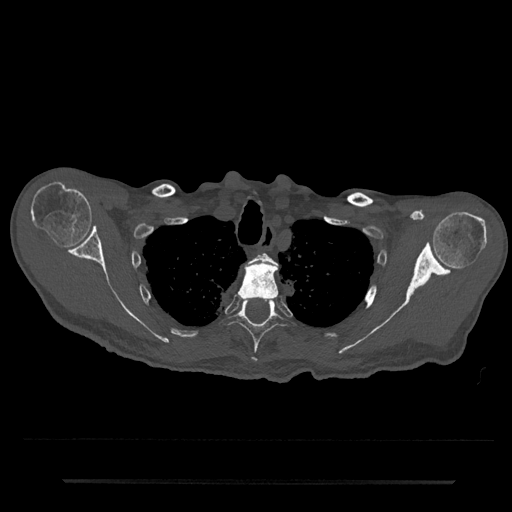
CT including the spine, one axial slice. Slice 637 of 797 in the series (ordered by position). Bone window (W 1800 / L 400 HU). 0.5 mm slice thickness. 512 × 512 image matrix, field of view 427 × 427 mm. Male patient, age 74 years. From the clinical record (not read from this slice): primary cancer: prostate.
Annotated regions visible in this slice (semi-automatic segmentation, software-assisted and operator-edited):
- T2 vertebra: bounding box (x1, y1, x2, y2) in pixels: (252, 253, 274, 263)
- T3 vertebra: (238, 258, 279, 301)
- T4 vertebra: (225, 298, 286, 362)